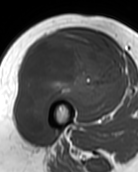
MRI of an extremity soft-tissue mass, one axial slice. Slice 56 of 99 in the series (ordered by position). MR volume resampled by the dataset authors to the PET/CT grid (not the native acquisition matrix). 3.27 mm slice thickness. 138 × 172 image matrix. Female patient. From the clinical record (not read from this slice): histological type: pleiomorphic undifferentiated sarcoma; grade: high; site of the primary tumour: right quadricep.
Structures marked on this image (expert contour drawn on MRI and transferred to this co-registered scan by the dataset authors):
- gross tumour volume including surrounding oedema: bounding box [x1, y1, x2, y2] px = [16, 32, 123, 136]
- gross tumour volume (mass): [16, 32, 123, 136]